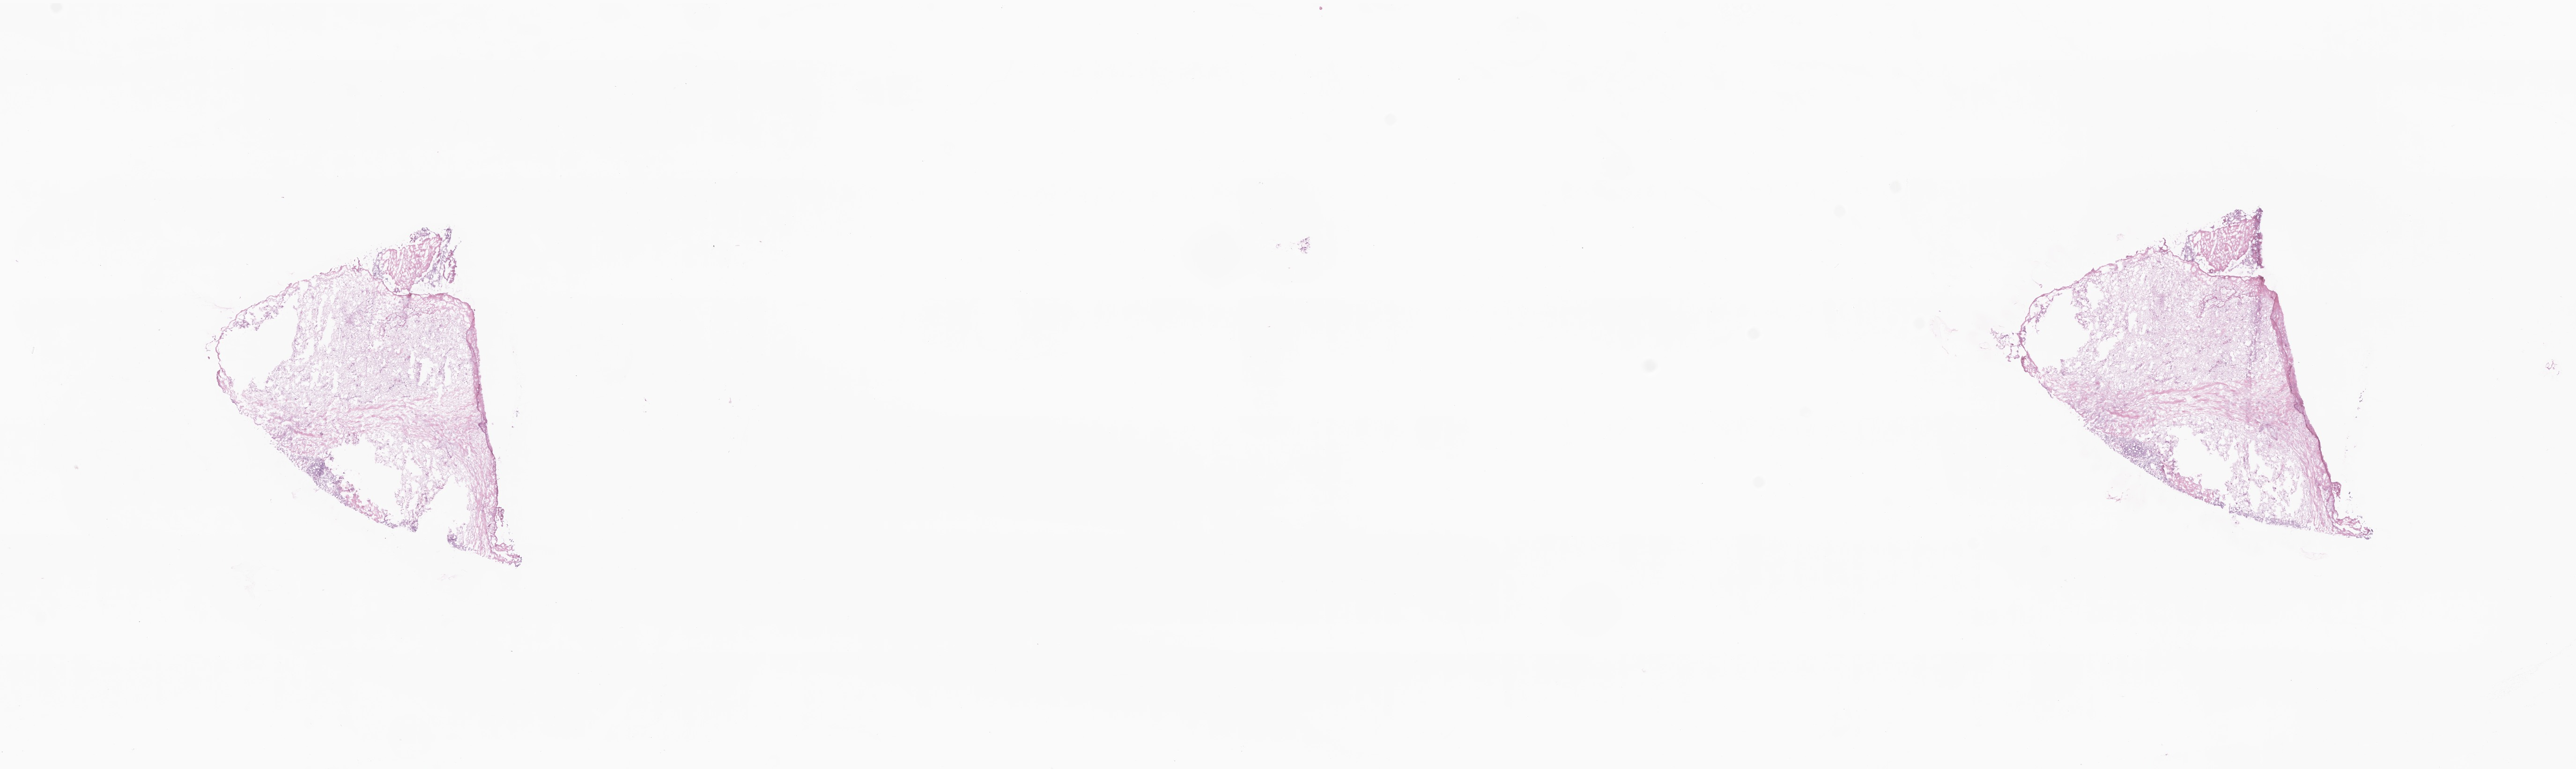
Haematoxylin and eosin whole-slide image, low-resolution overview of the scanned area, about 23.2 x 6.9 mm, frozen section (tissue freezing medium), metastatic tumor tissue, resected from lymph node. Male, age 66 years at initial diagnosis. Composition of this section per pathologist review: tumor cells 70%, tumor nuclei 70%, stromal cells 30%, necrosis 0%, normal cells 0%. Infiltration values recorded for this section: lymphocyte infiltration 9%, monocyte infiltration 3%, neutrophil infiltration 7%.
Patient diagnosis (primary): Malignant melanoma, NOS. Section: bottom of the tissue portion.